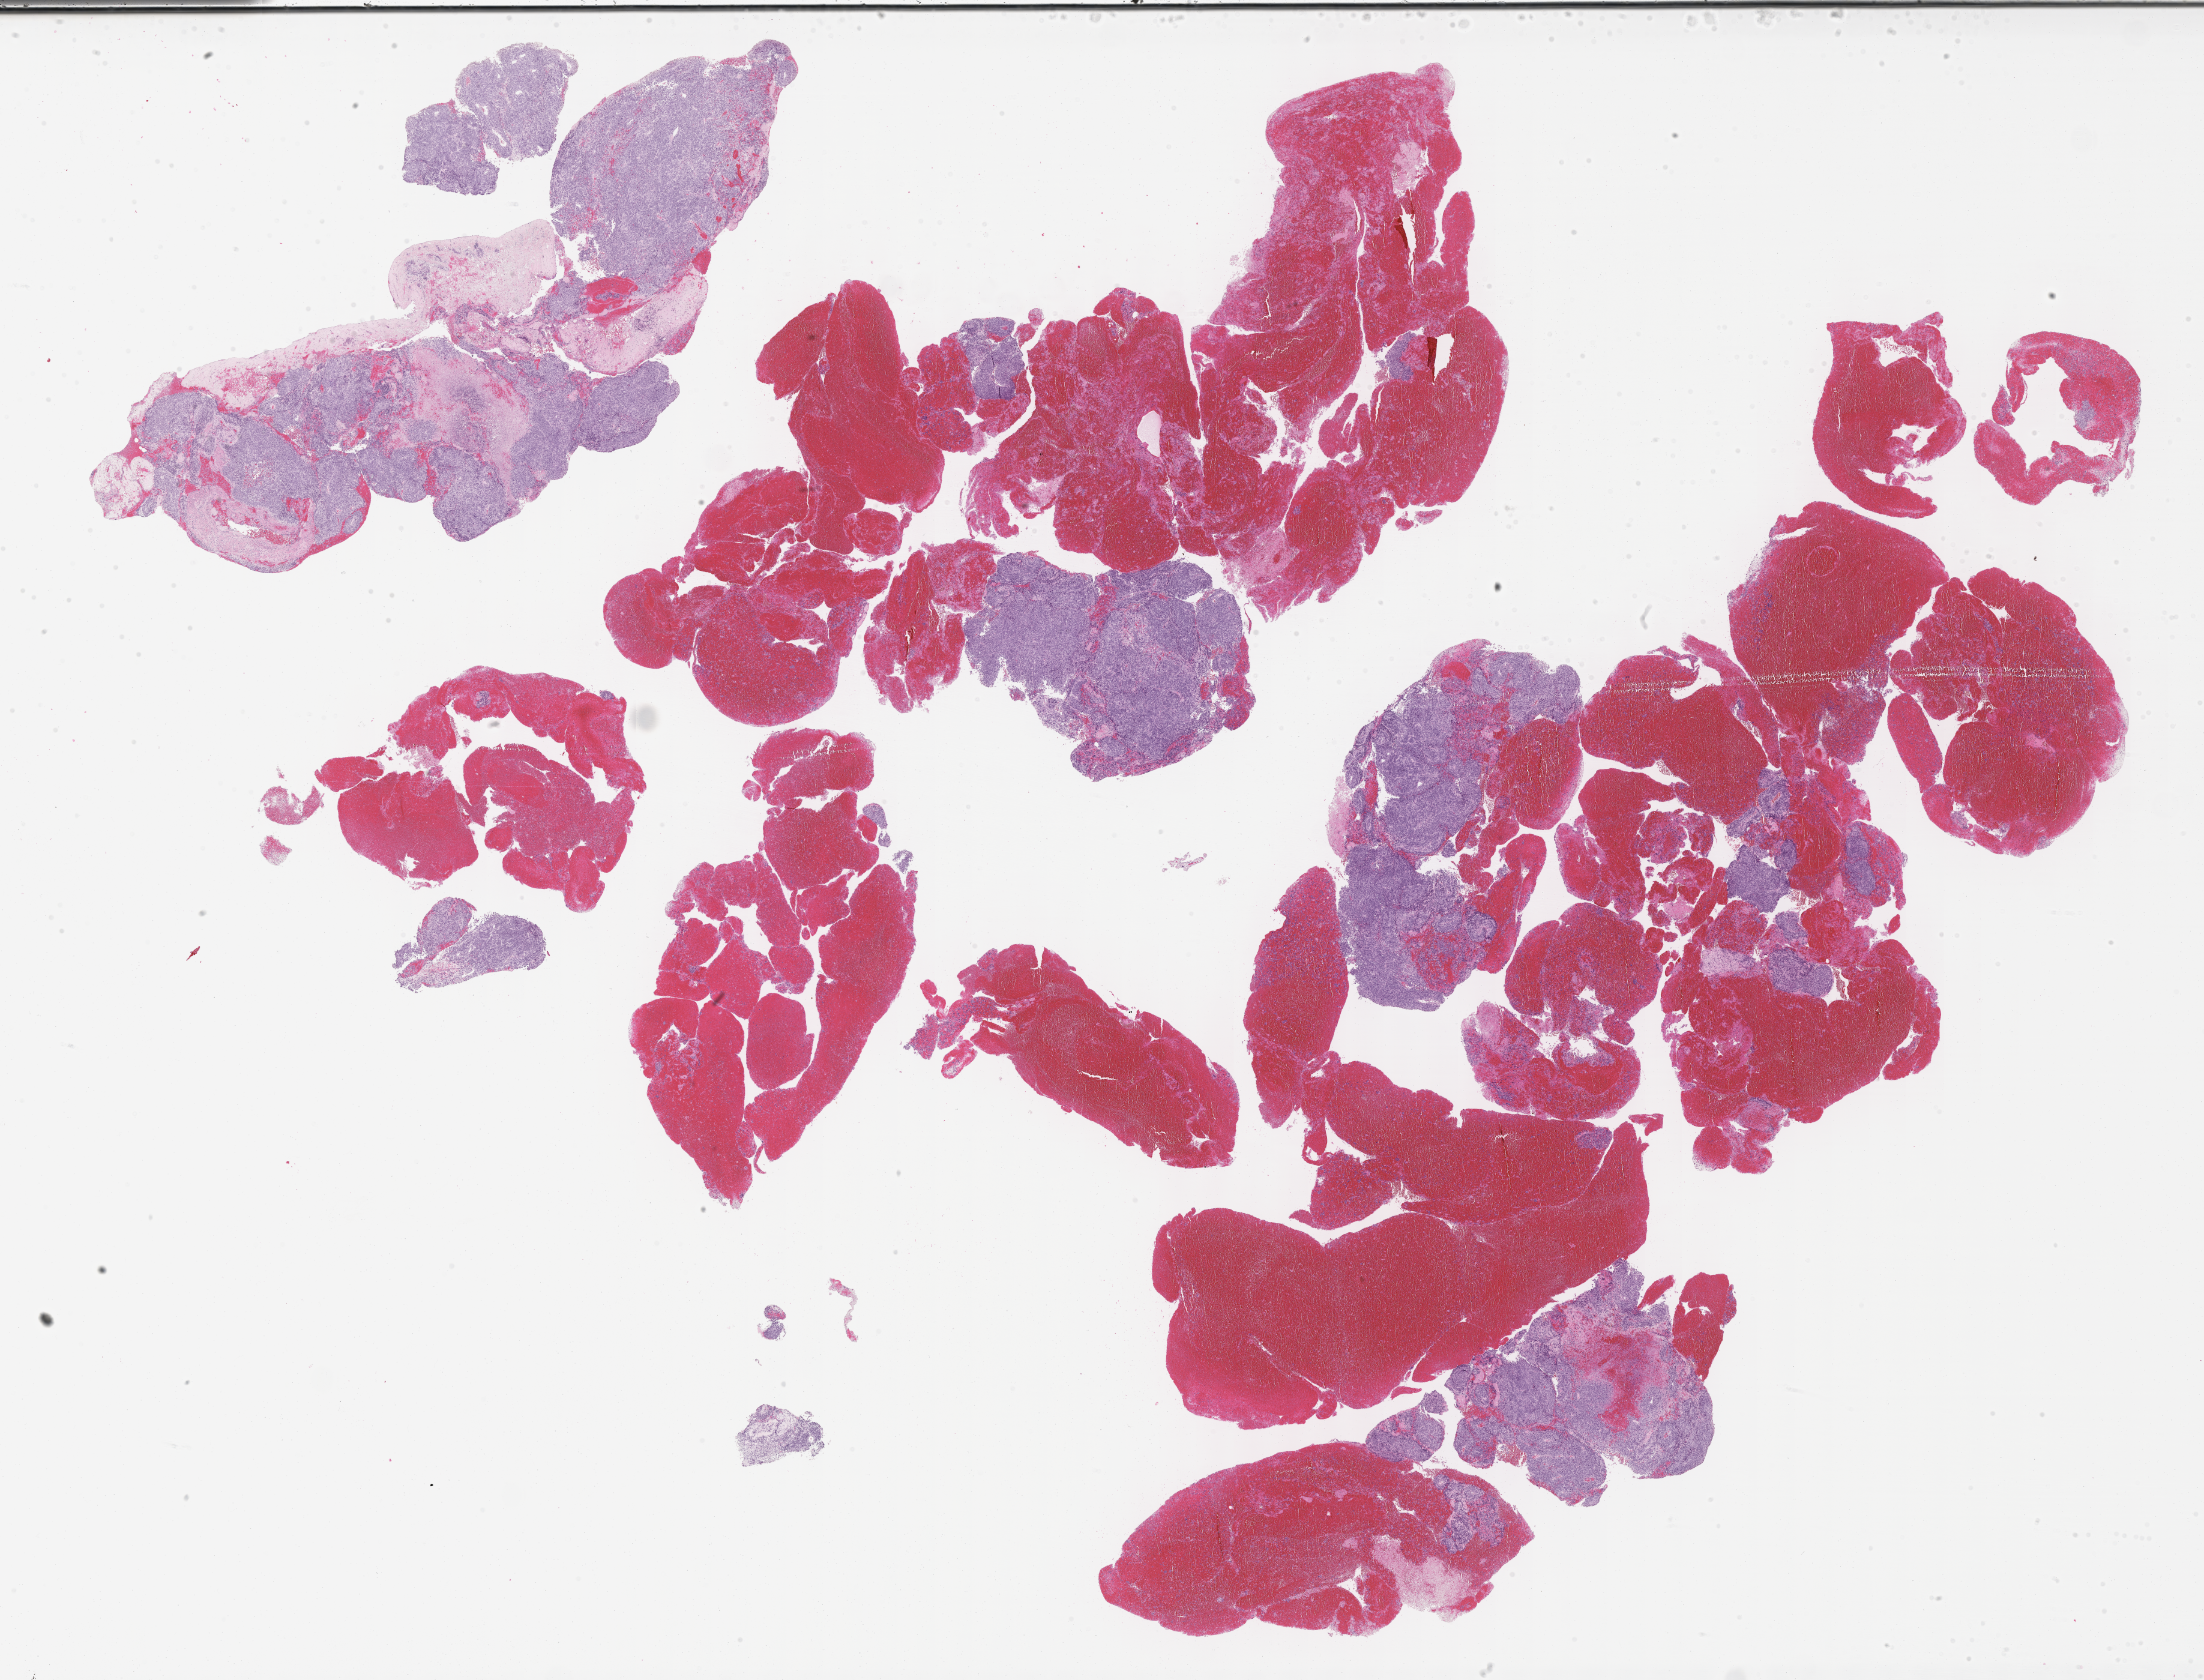
Haematoxylin and eosin whole-slide image of tumor tissue, whole scanned area (about 29.7 x 22.6 mm) shown as a low-resolution overview; FFPE section; sample anatomic site: pelvis. Patient: female, age 6.2 years at diagnosis.
- metastatic status at presentation (as recorded): metastatic (confirmed)
- stage (as recorded): 4
- diagnosis: rhabdomyosarcoma; histological classification: embryonal rhabdomyosarcoma